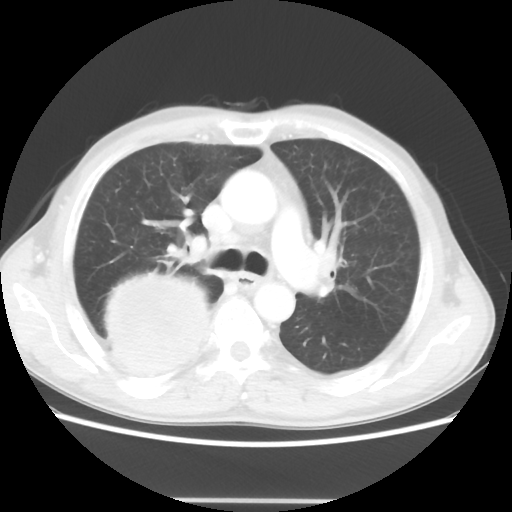
Chest CT, one axial slice. Position 31 of 48 along the scan axis. Reconstruction kernel STANDARD. 100 kVp. Lung window (W 1500 / L -600 HU). 512 × 512 image matrix, field of view 361 × 361 mm. Male patient, age 66 years. From the clinical record (not read from this slice): clinical TNM (as recorded): T4 N1 M1; histopathological grade: G3.
Outlined on this slice (rectangle marked by the reading radiologist):
- lung tumour (recorded histology: small cell carcinoma): box from (x=98, y=271) to (x=213, y=383) px